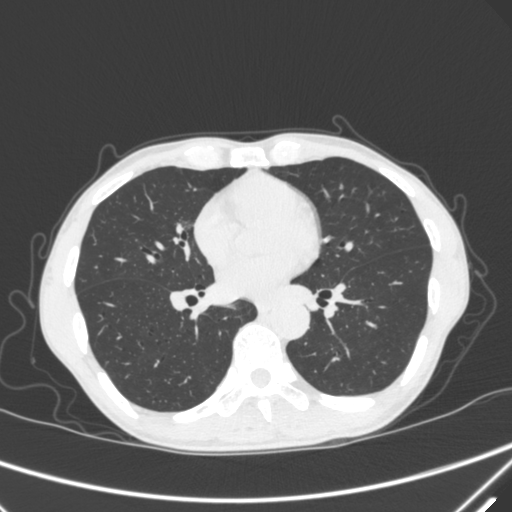
Chest CT, one axial slice; position 158 of 340 along the scan axis; lung window (W 1500 / L -600 HU); 512 × 512 image matrix. Male patient, age 67 years. From the clinical record (not read from this slice): clinical TNM (as recorded): T1c N0 M0; histopathological grade: G1-2.
Structures marked on this image (bounding box drawn by a radiologist):
- lung tumour (recorded histology: adenocarcinoma): bounding box [x1, y1, x2, y2] px = [172, 213, 195, 240]